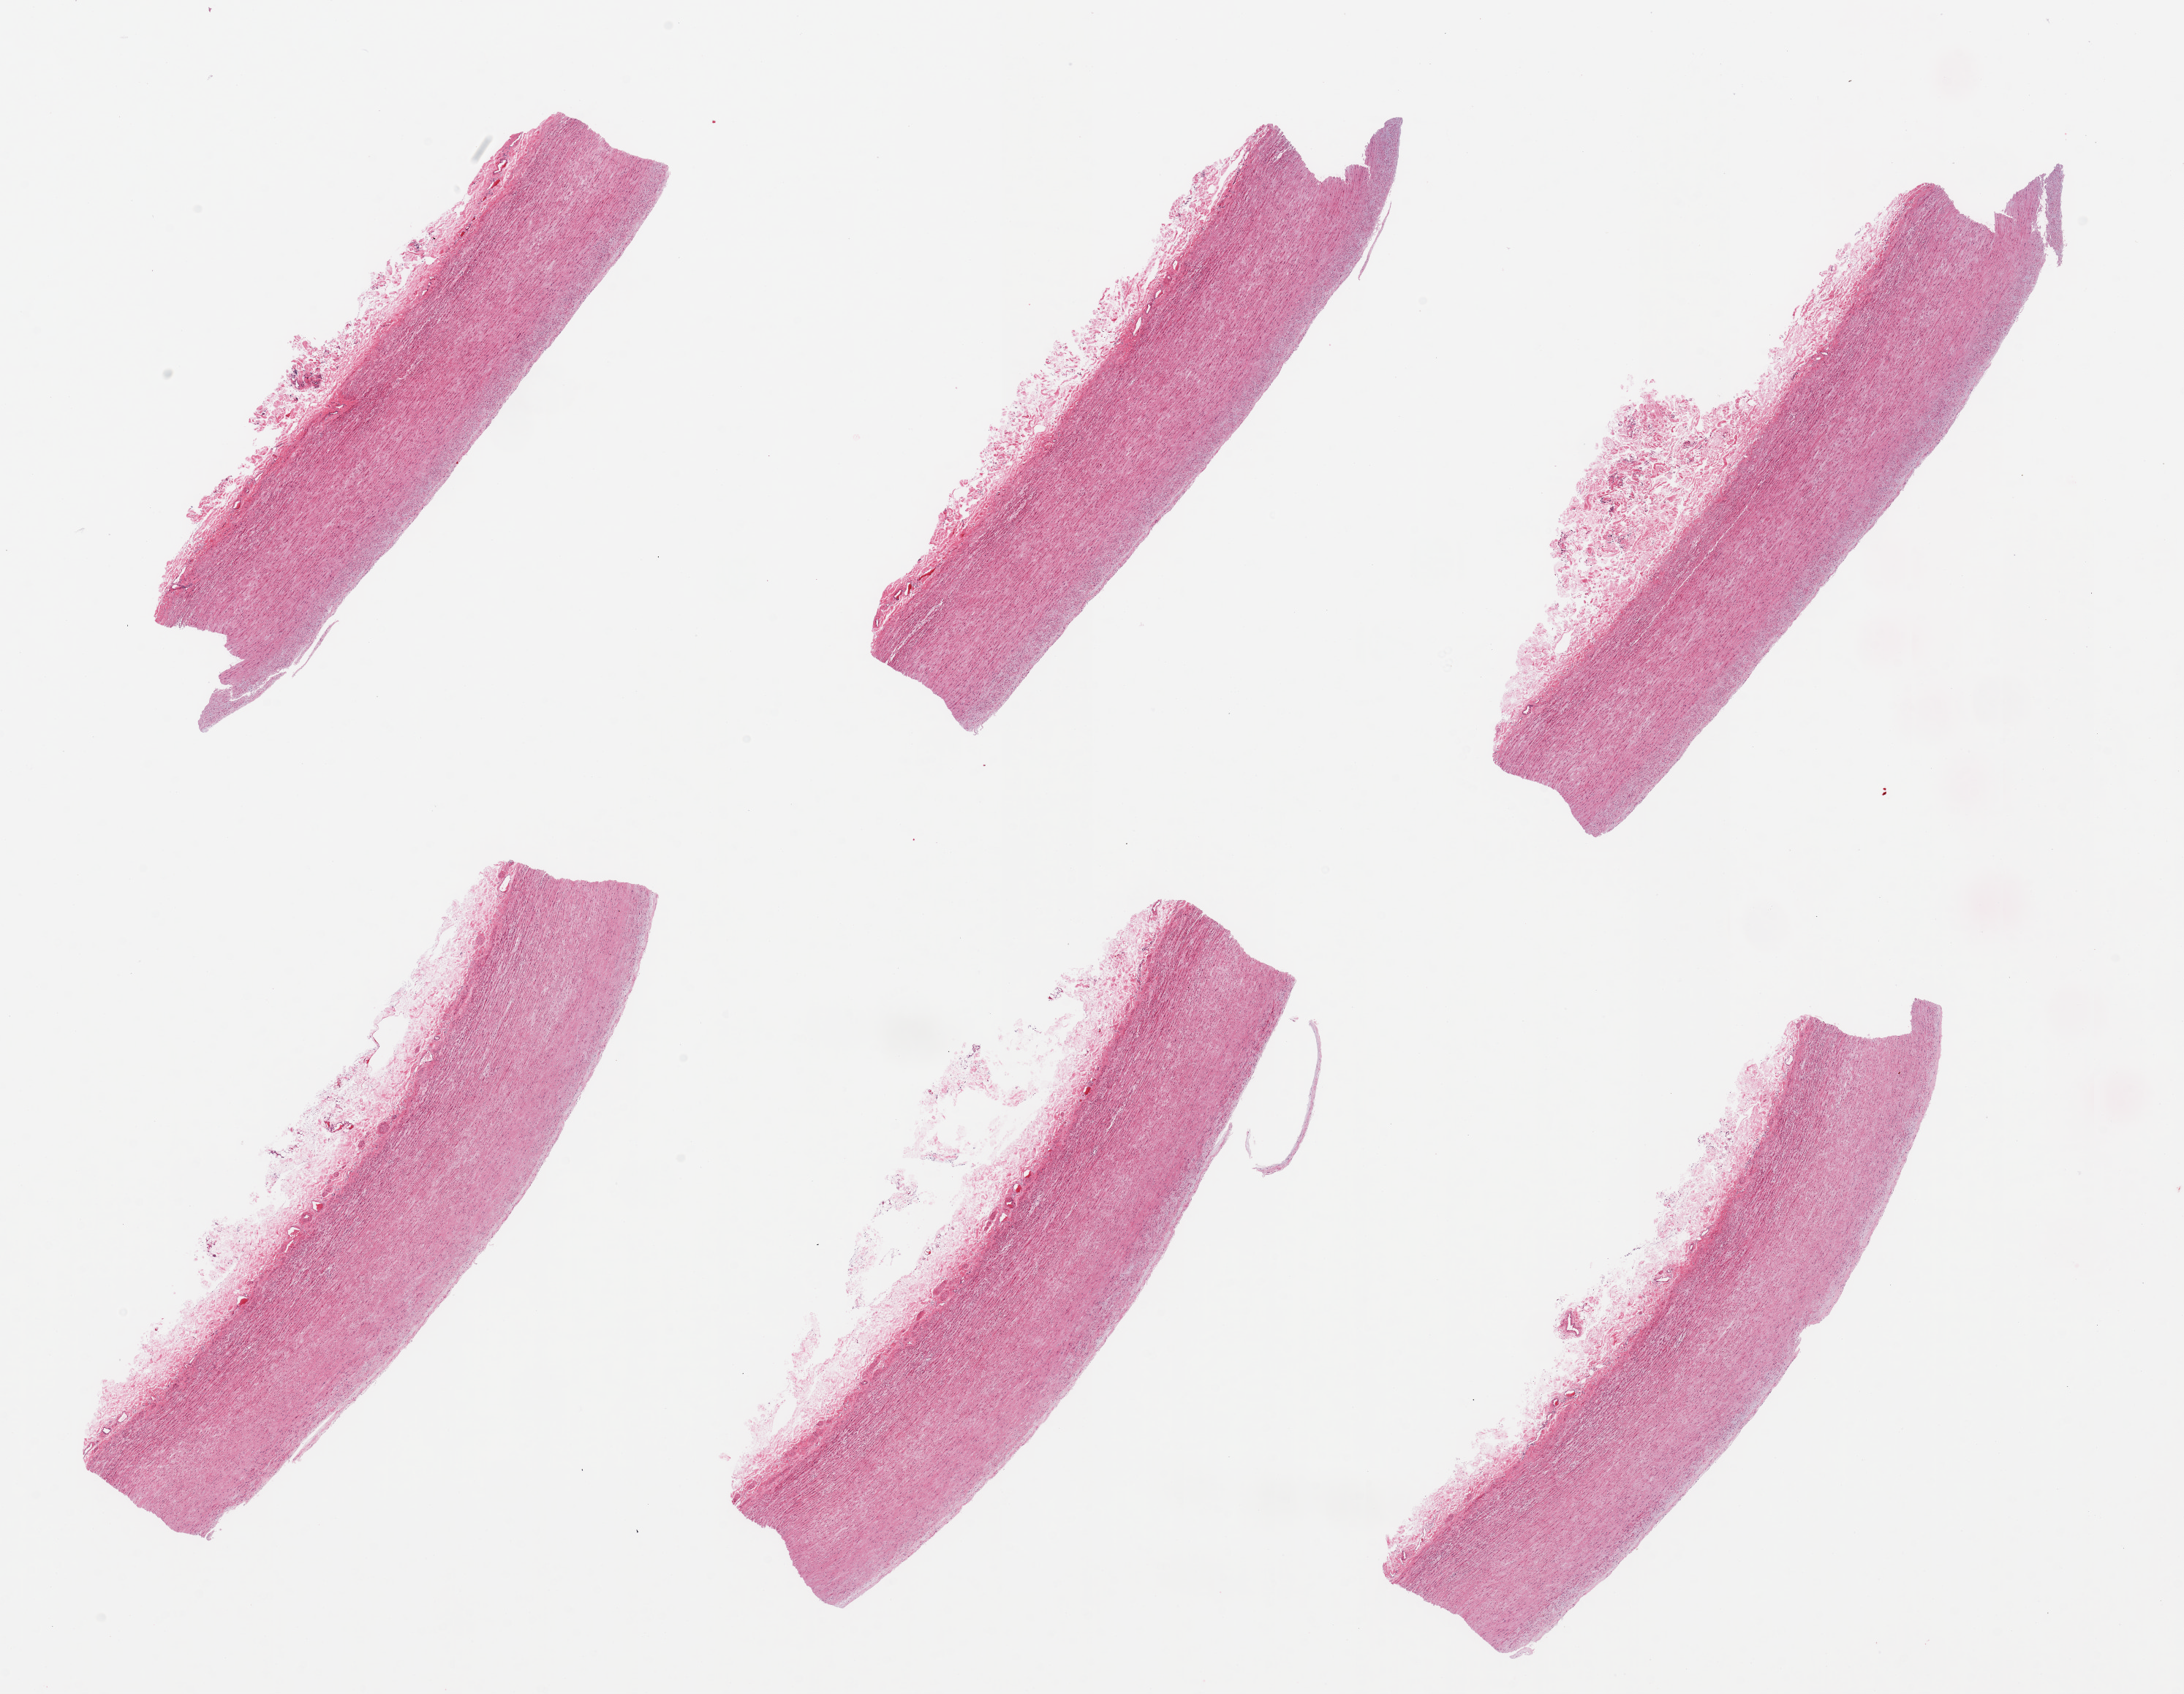
H&E whole-slide image — shown as a low-resolution overview of the whole scanned area (about 23.6 x 18.3 mm), PAXgene-fixed paraffin-embedded (PFPE) section, section of aorta (target tissue), tissue donor sample. Male donor.
Pathologist's review note for this sample: 6 pieces, atherosis up to ~0.25mm.